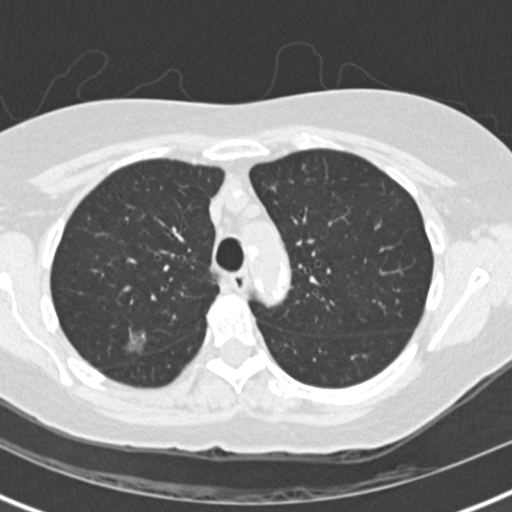
Low-dose screening chest CT, one axial slice. Position 103 of 147 along the scan axis. 120 kVp. Lung window (W 1500 / L -600 HU). 2 mm slice thickness. 512 × 512 image matrix, field of view 300 × 300 mm.
Structures marked on this image (outlined manually by an expert reader):
- lesion 1 (tumor, upper lobe of right lung): box from (x=128, y=331) to (x=148, y=354) px